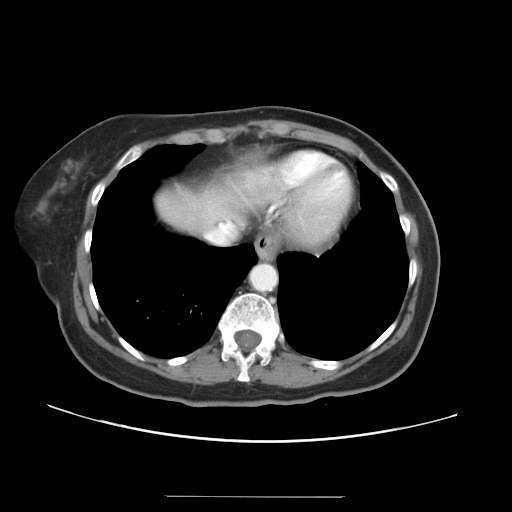
Contrast-enhanced abdominal CT, one axial slice; slice 31 of 34 in the series (ordered by position); reconstruction kernel STANDARD; 120 kVp; soft-tissue window (W 400 / L 40 HU); 512 × 512 image matrix, field of view 382 × 382 mm. Female patient, age 69 years. Case-level facts recorded for this patient, not image findings: diagnosis: colorectal cancer liver metastases, imaged before liver resection; multiple liver metastases: yes; largest metastasis: 1.4 cm.
Outlined on this slice (expert manual segmentation):
- hepatic veins: bounding box [x1, y1, x2, y2] px = [207, 154, 331, 244]
- liver: [156, 153, 282, 235]
- planned liver remnant (the part of the liver to remain after resection): [156, 153, 283, 235]